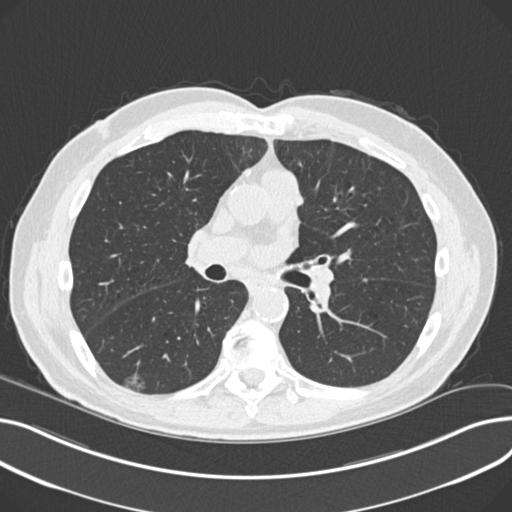
Low-dose screening chest CT, one axial slice. Slice 121 of 230 in the series (ordered by position). Reconstruction kernel B30f. Lung window (W 1500 / L -600 HU). 512 × 512 image matrix.
Annotated regions visible in this slice (outlined manually by an expert reader):
- lesion 1 (nodule, lower lobe of right lung): bounding box [x1, y1, x2, y2] px = [124, 374, 145, 392]